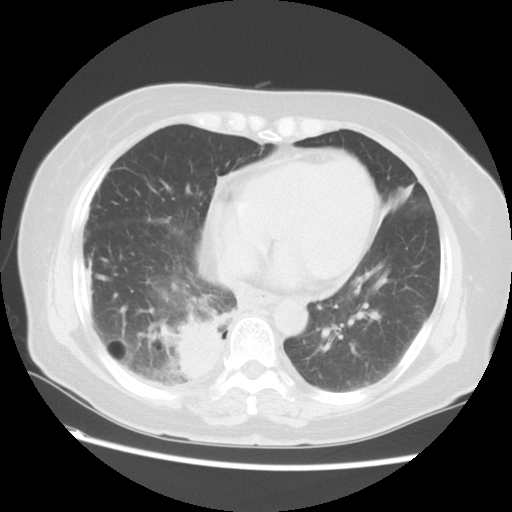
Chest CT, one axial slice. Position 24 of 57 along the scan axis. 120 kVp. Lung window (W 1500 / L -600 HU). 5 mm slice thickness. 512 × 512 image matrix, field of view 350 × 350 mm. Female patient, age 69 years. From the clinical record (not read from this slice): clinical TNM (as recorded): T2 N1 M1a.
Outlined on this slice (bounding box drawn by a radiologist):
- lung tumour (recorded histology: adenocarcinoma): box from (x=168, y=308) to (x=226, y=391) px